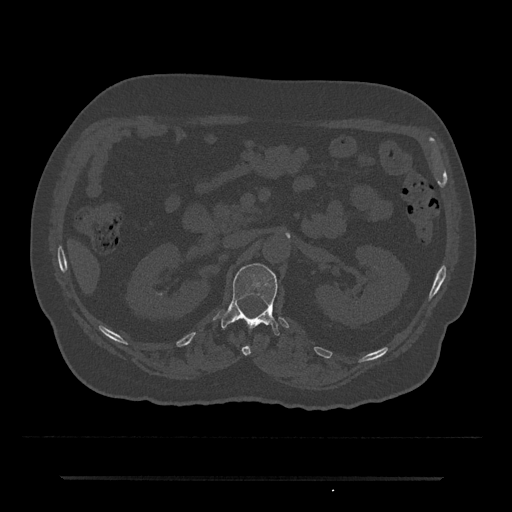
CT including the spine, one axial slice. Position 77 of 797 along the scan axis. 120 kVp. Bone window (W 1800 / L 400 HU). 512 × 512 image matrix, field of view 437 × 437 mm. Patient: male, 69 years. From the clinical record (not read from this slice): primary cancer: prostate.
Annotated regions visible in this slice (semi-automatically segmented with operator editing):
- L1 vertebra: bounding box [x1, y1, x2, y2] px = [221, 263, 280, 336]
- T12 vertebra: [242, 345, 251, 355]